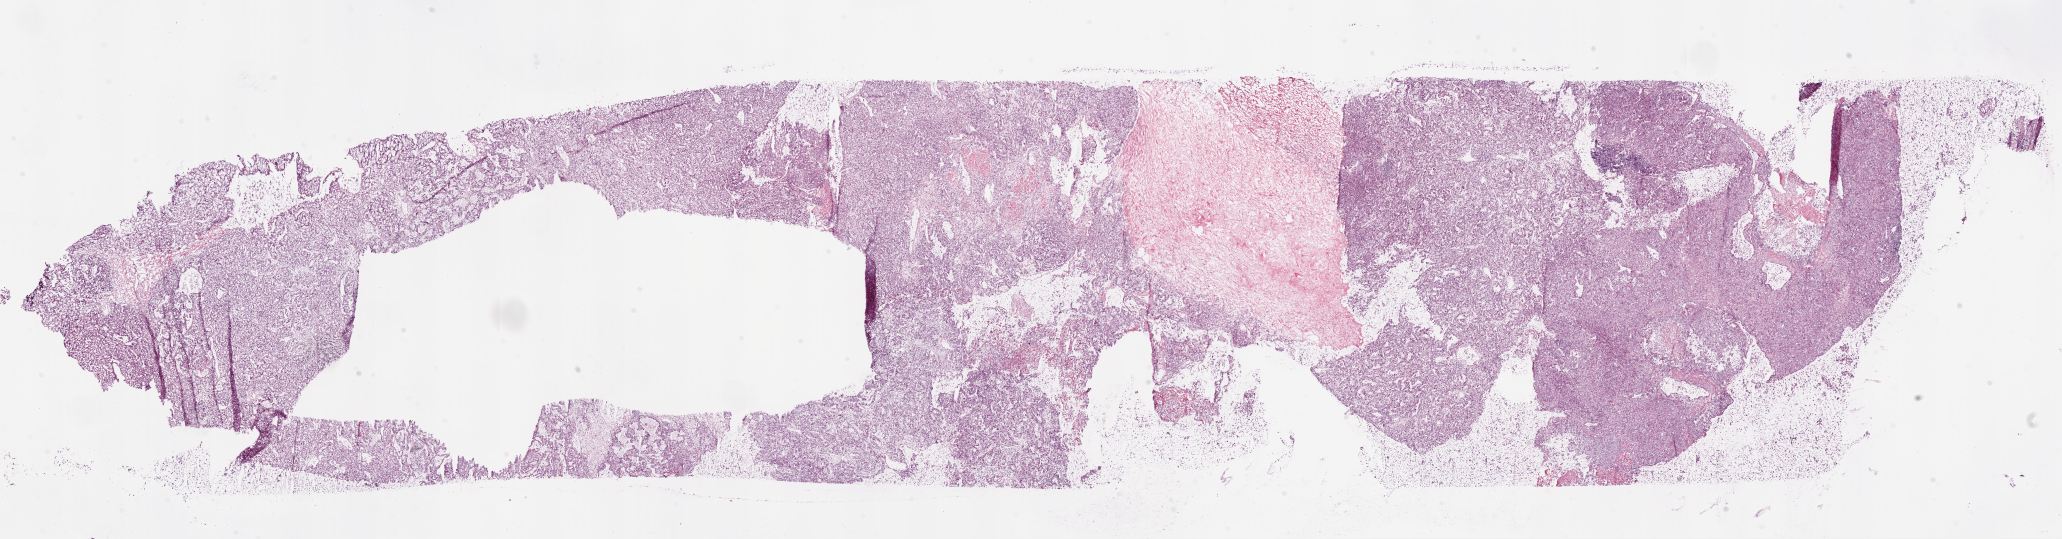
Digitized H&E-stained tissue section (whole slide), whole scanned area (about 33.1 x 8.7 mm, slide scanned at 20x) shown as a low-resolution overview; frozen section; primary tumour sample from the kidney. Patient: male, age at initial diagnosis 49 years. Histologic grade: G2 (moderately differentiated). Composition of this section per pathologist review: tumour cells 88%, tumour nuclei 80%, normal cells 0%, stromal cells 10%, necrosis 2%.
Laterality: right. Lymph nodes positive (case pathology): 3 of 10 examined. AJCC pathologic stage: III. Histologic diagnosis: Clear cell adenocarcinoma, NOS.